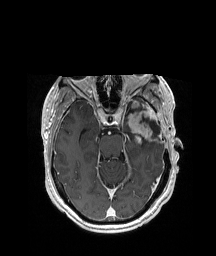
Brain MRI from a brain-tumour surgery series, one axial slice. Position 128 of 208 along the scan axis. T1-weighted post-contrast. 1 mm slice thickness. 216 × 256 image matrix. Case-level facts recorded for this patient, not image findings: histopathology: Glioblastoma; WHO grade: 4; IDH mutation: no.
Annotated regions visible in this slice (expert manual segmentation):
- previous resection cavity: bounding box [x1, y1, x2, y2] px = [139, 115, 160, 135]
- tumour: [123, 99, 158, 144]